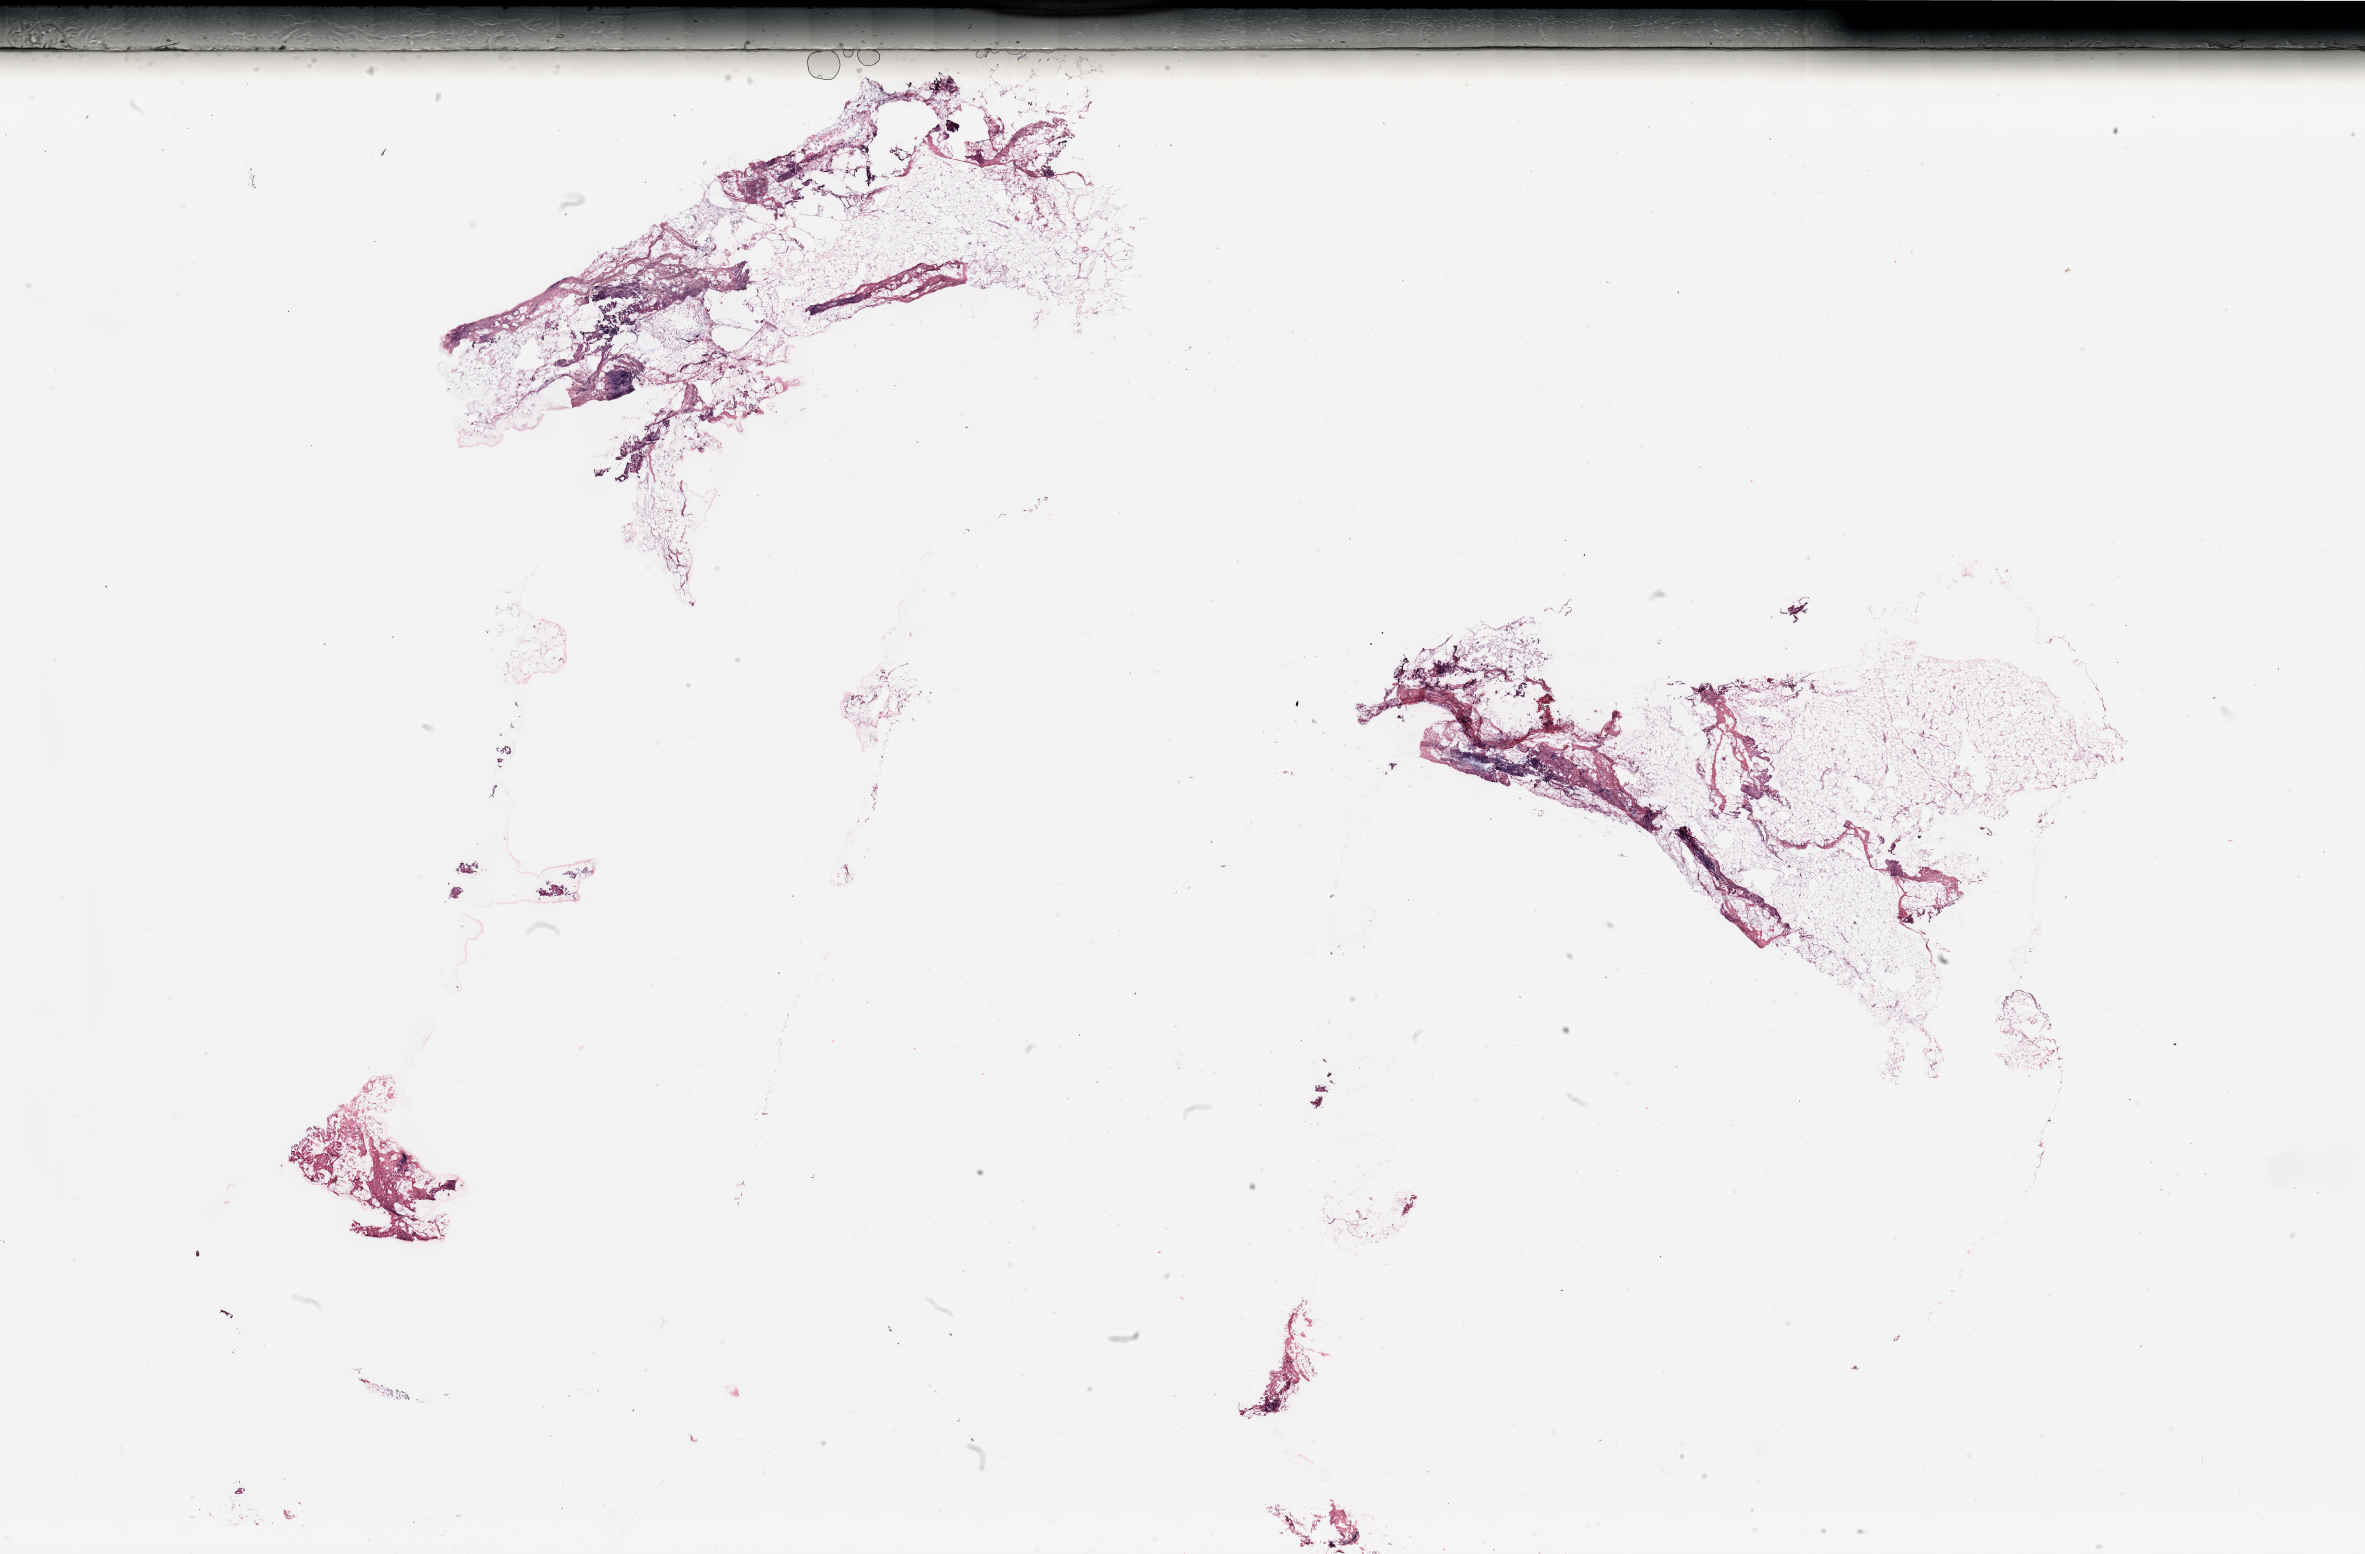
Hematoxylin and eosin (H&E) stained whole-slide image, shown as a low-resolution overview of the whole scanned area (about 37.4 x 24.6 mm, from a 20x scan). Tumour tissue sample, breast. Patient: female, age 55 years.
Histologic diagnosis: Infiltrating duct carcinoma, NOS. AJCC pathologic stage: IIA.